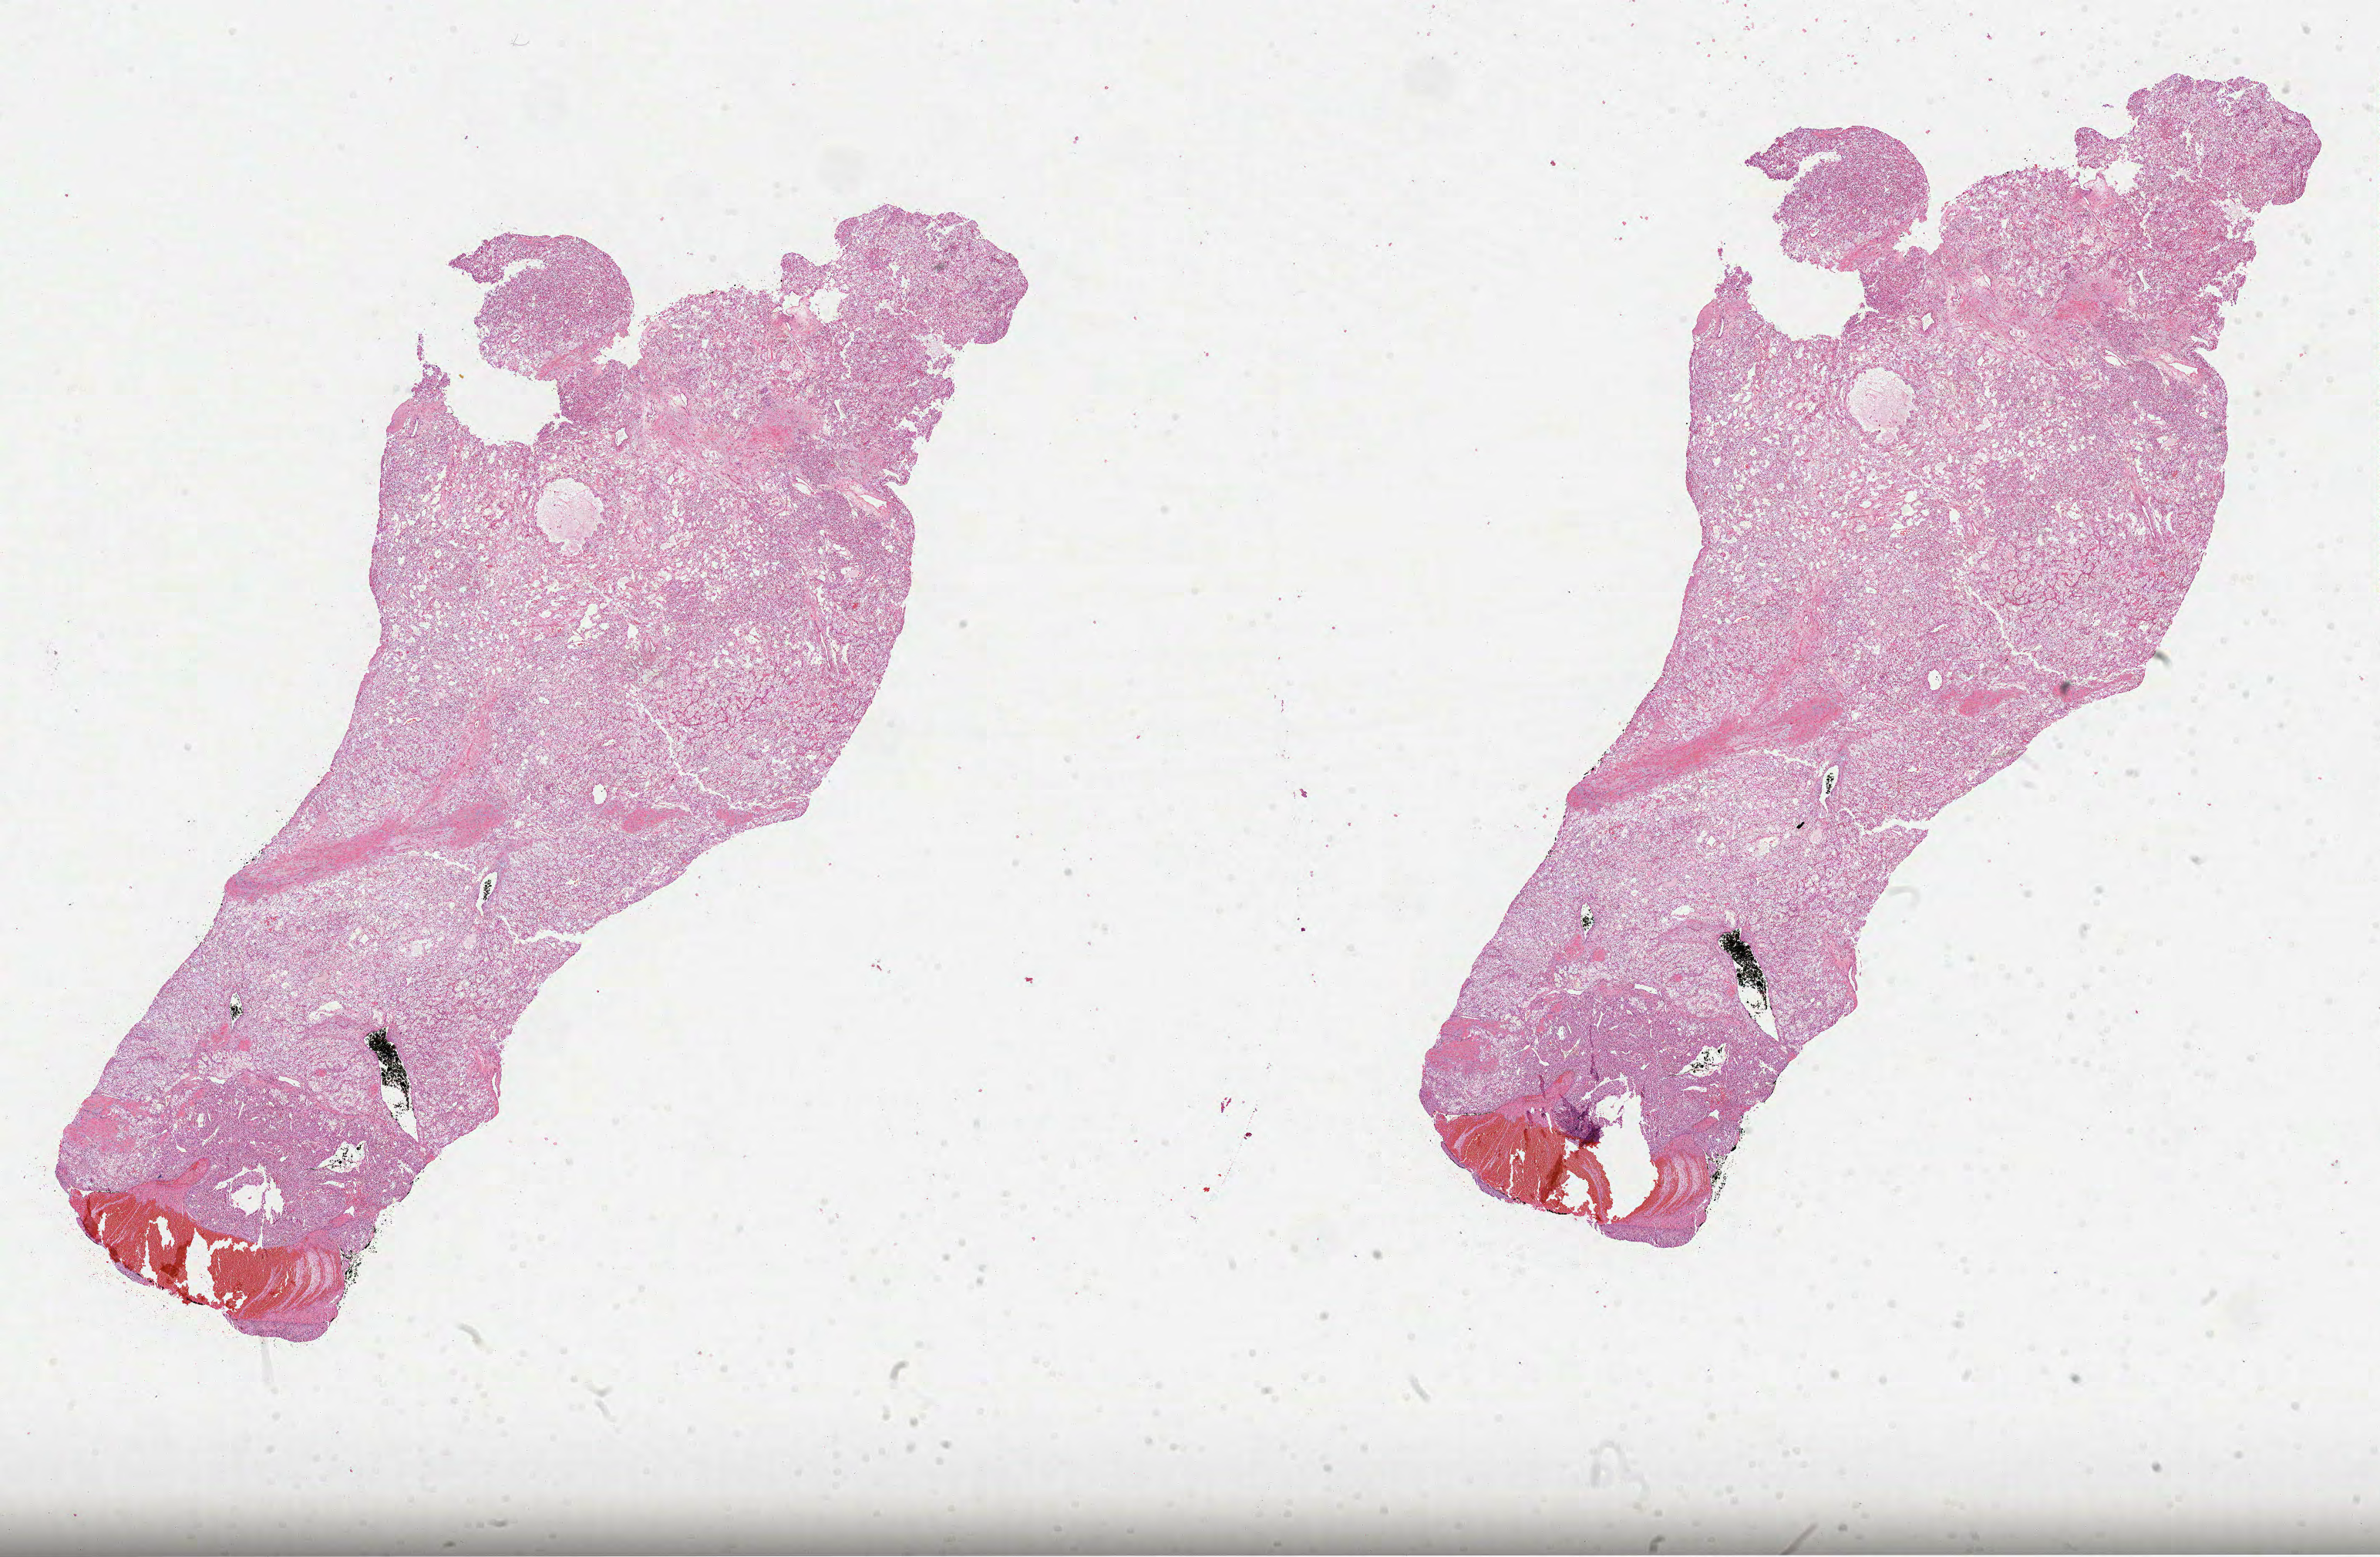
Digitized H&E-stained tissue section (whole slide) — whole scanned area (about 24.9 x 16.3 mm, from a 40x scan) shown as a low-resolution overview. Formalin-fixed paraffin-embedded (FFPE) diagnostic section. Primary tumour sample from the kidney. Patient: male, age at initial diagnosis 57 years.
Diagnosis: Clear cell adenocarcinoma, NOS.